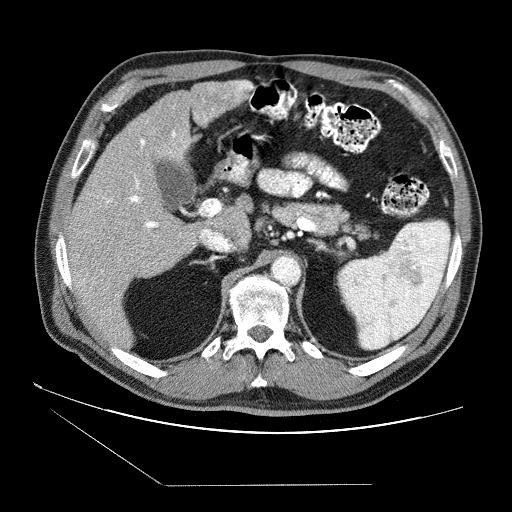
Contrast-enhanced abdominal CT (liver protocol), one axial slice; position 45 of 87 along the scan axis; soft-tissue window (W 400 / L 40 HU); 512 × 512 image matrix, field of view 400 × 400 mm. From the clinical record (not read from this slice): diagnosis: hepatocellular carcinoma (patient treated with transarterial chemoembolisation; whether this scan precedes or follows treatment is not stated here); TNM stage (as recorded): Stage-II; Child-Pugh class: B; tumour differentiation: no biopsy; tumour size: 2.6 cm.
Structures marked on this image (semi-automatically segmented with operator editing):
- liver parenchyma outside the tumour (the mass and vessels are separate outlines, so this box may not span the whole liver): bounding box [x1, y1, x2, y2] px = [66, 80, 253, 346]
- liver vessels: [68, 81, 253, 296]